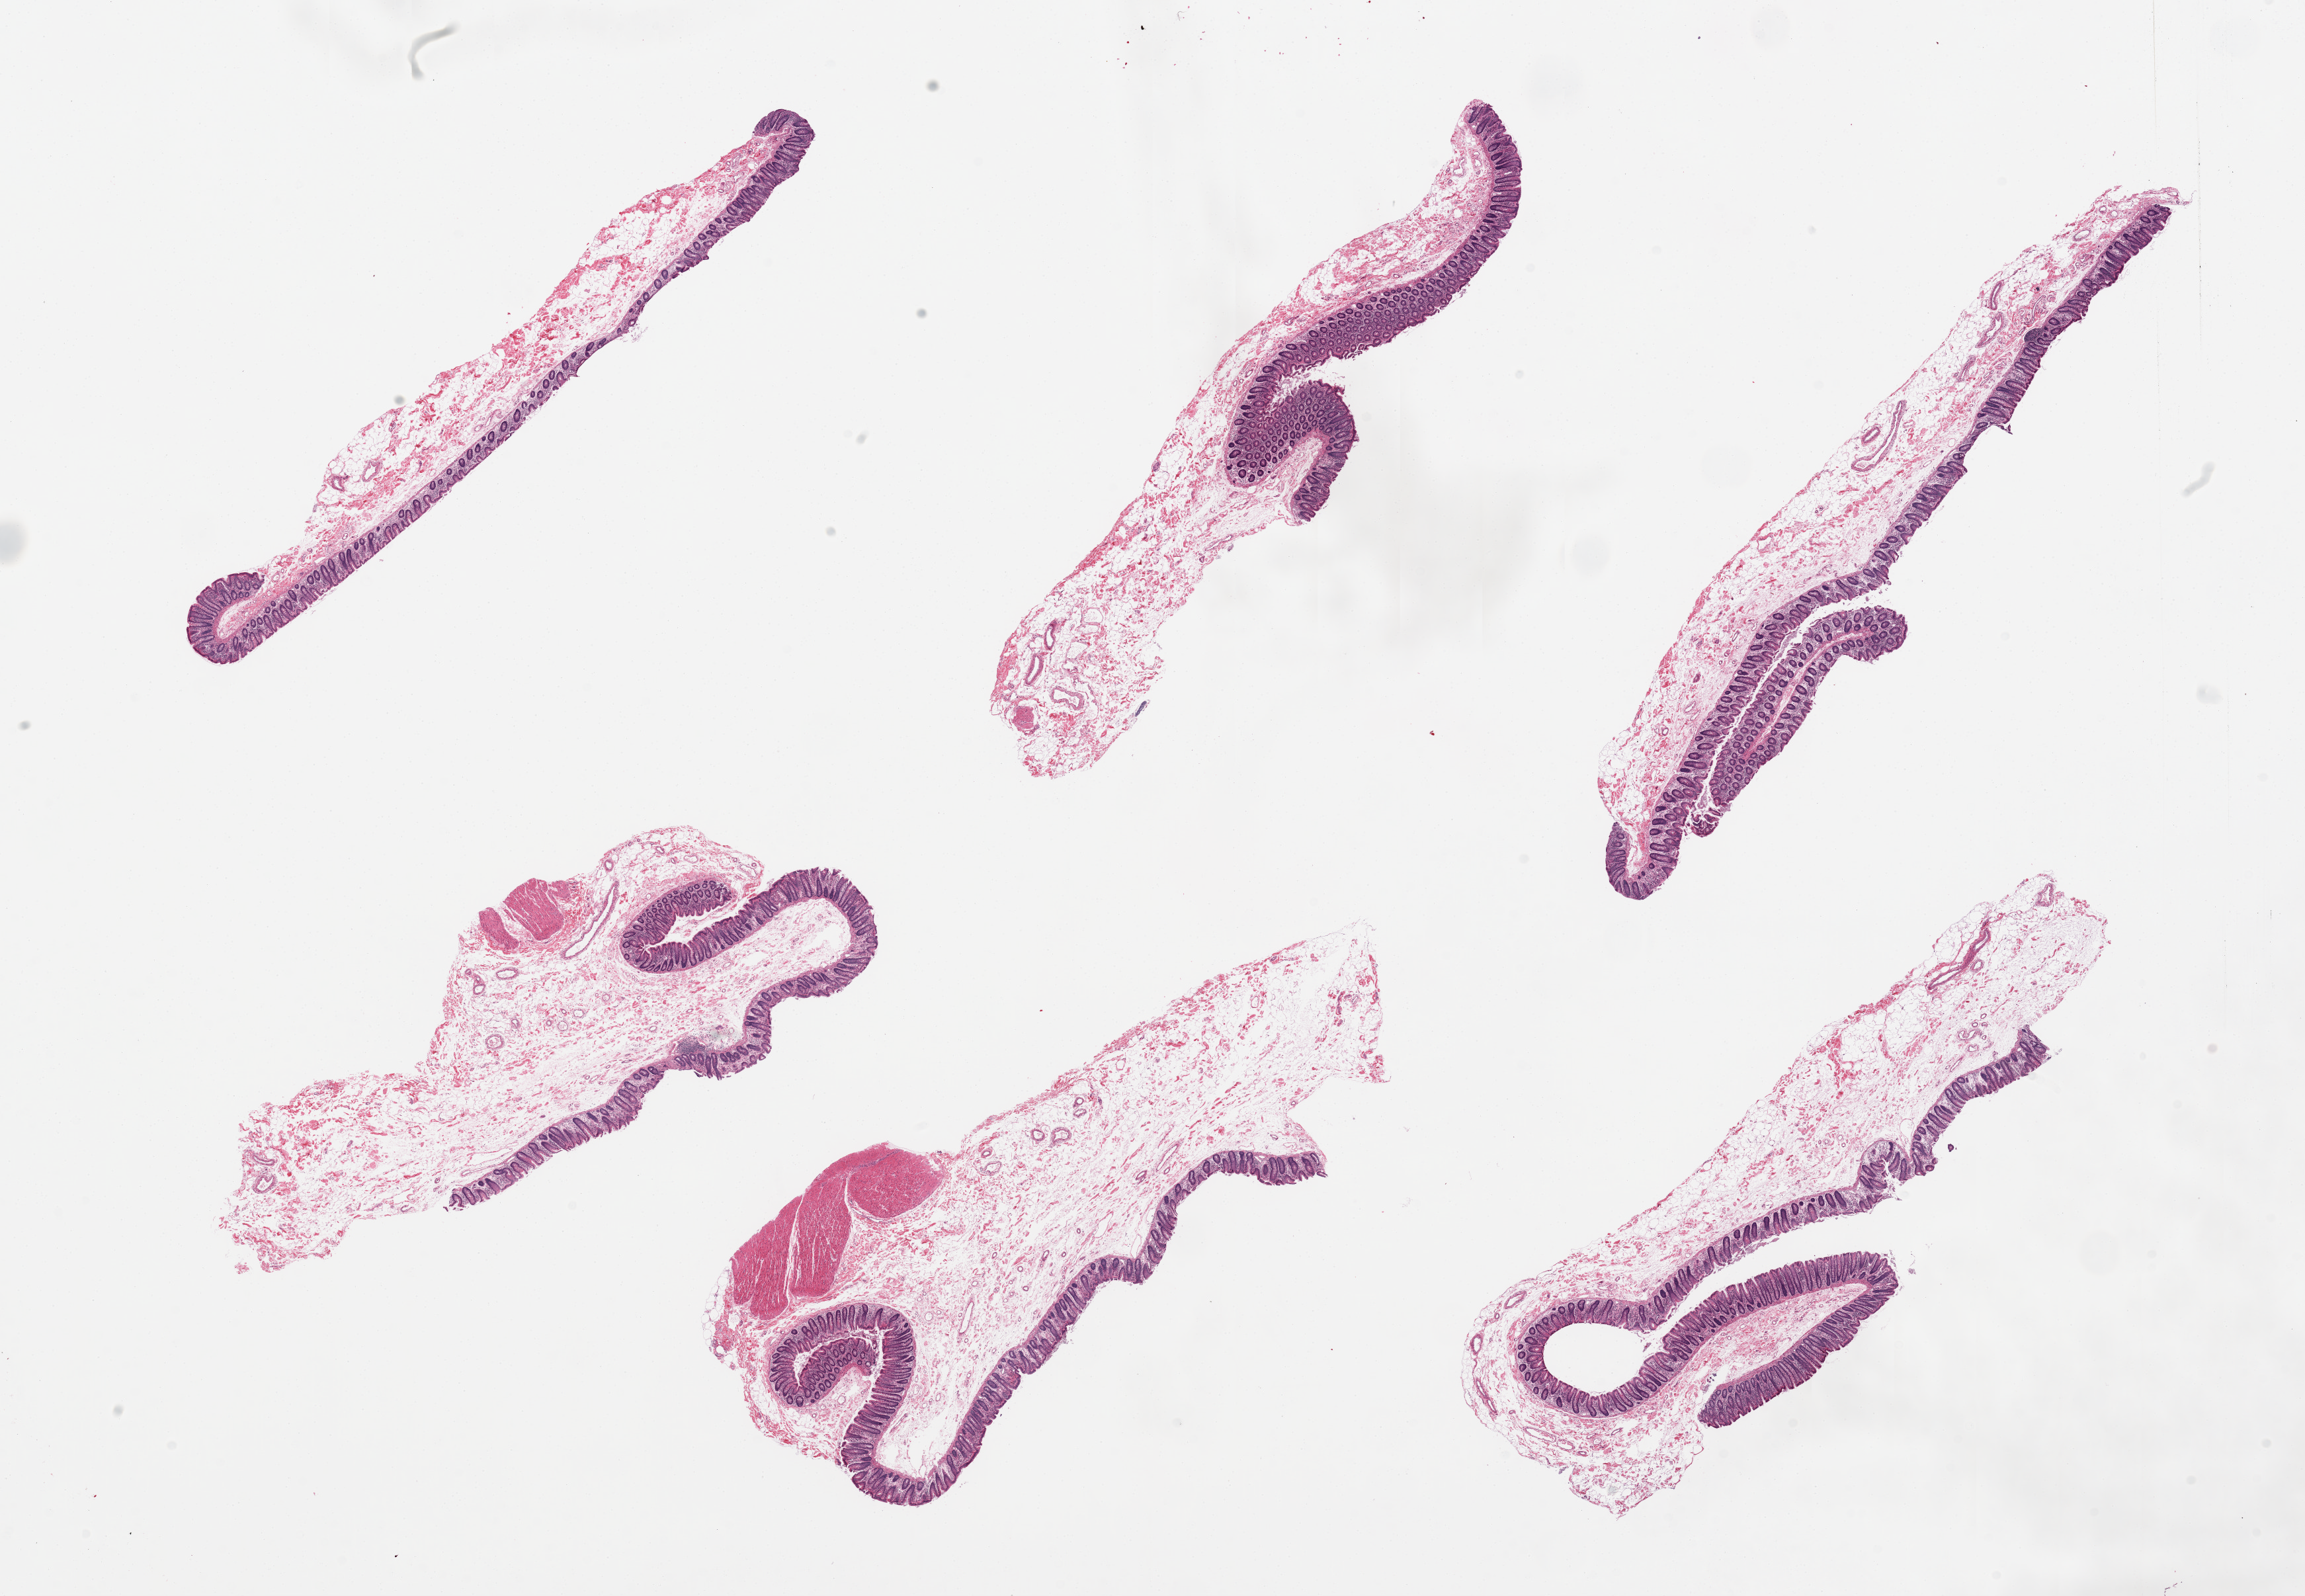
Digitized hematoxylin and eosin (H&E)-stained section, brightfield — a low-resolution overview of the entire scanned area, about 27.6 x 19.1 mm; PAXgene-fixed paraffin-embedded (PFPE) section; section of transverse colon (target tissue); donor tissue sample.
Reviewer comment on this tissue sample: 6 pieces, predominantly mucosa and submucosa with small portion of muscularis, edema.